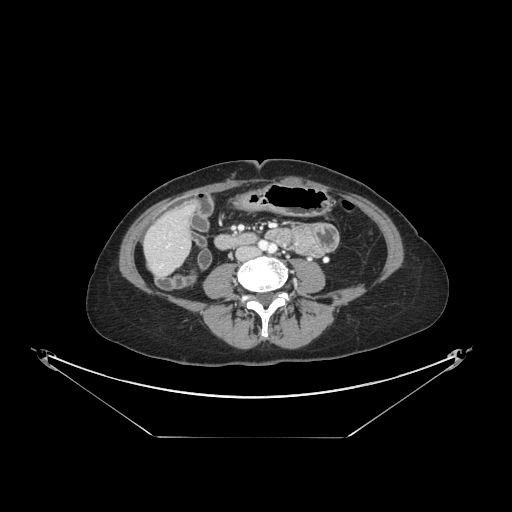
Contrast-enhanced abdominal CT, one axial slice. Position 29 of 148 along the scan axis. Reconstruction kernel STANDARD. 120 kVp. Intravenous contrast given. Soft-tissue window (W 400 / L 40 HU). 2.5 mm slice thickness. 512 × 512 image matrix, field of view 500 × 500 mm. Female patient, age 73 years. From the clinical record (not read from this slice): diagnosis: colorectal cancer liver metastases, imaged before liver resection; multiple liver metastases: no; largest metastasis: 1 cm; disease in both lobes: no.
Outlined on this slice (outlined manually by an expert reader):
- liver: bounding box <146,209,191,274> (left, top, right, bottom; pixels)
- planned liver remnant (the part of the liver to remain after resection): <164,208,189,236>